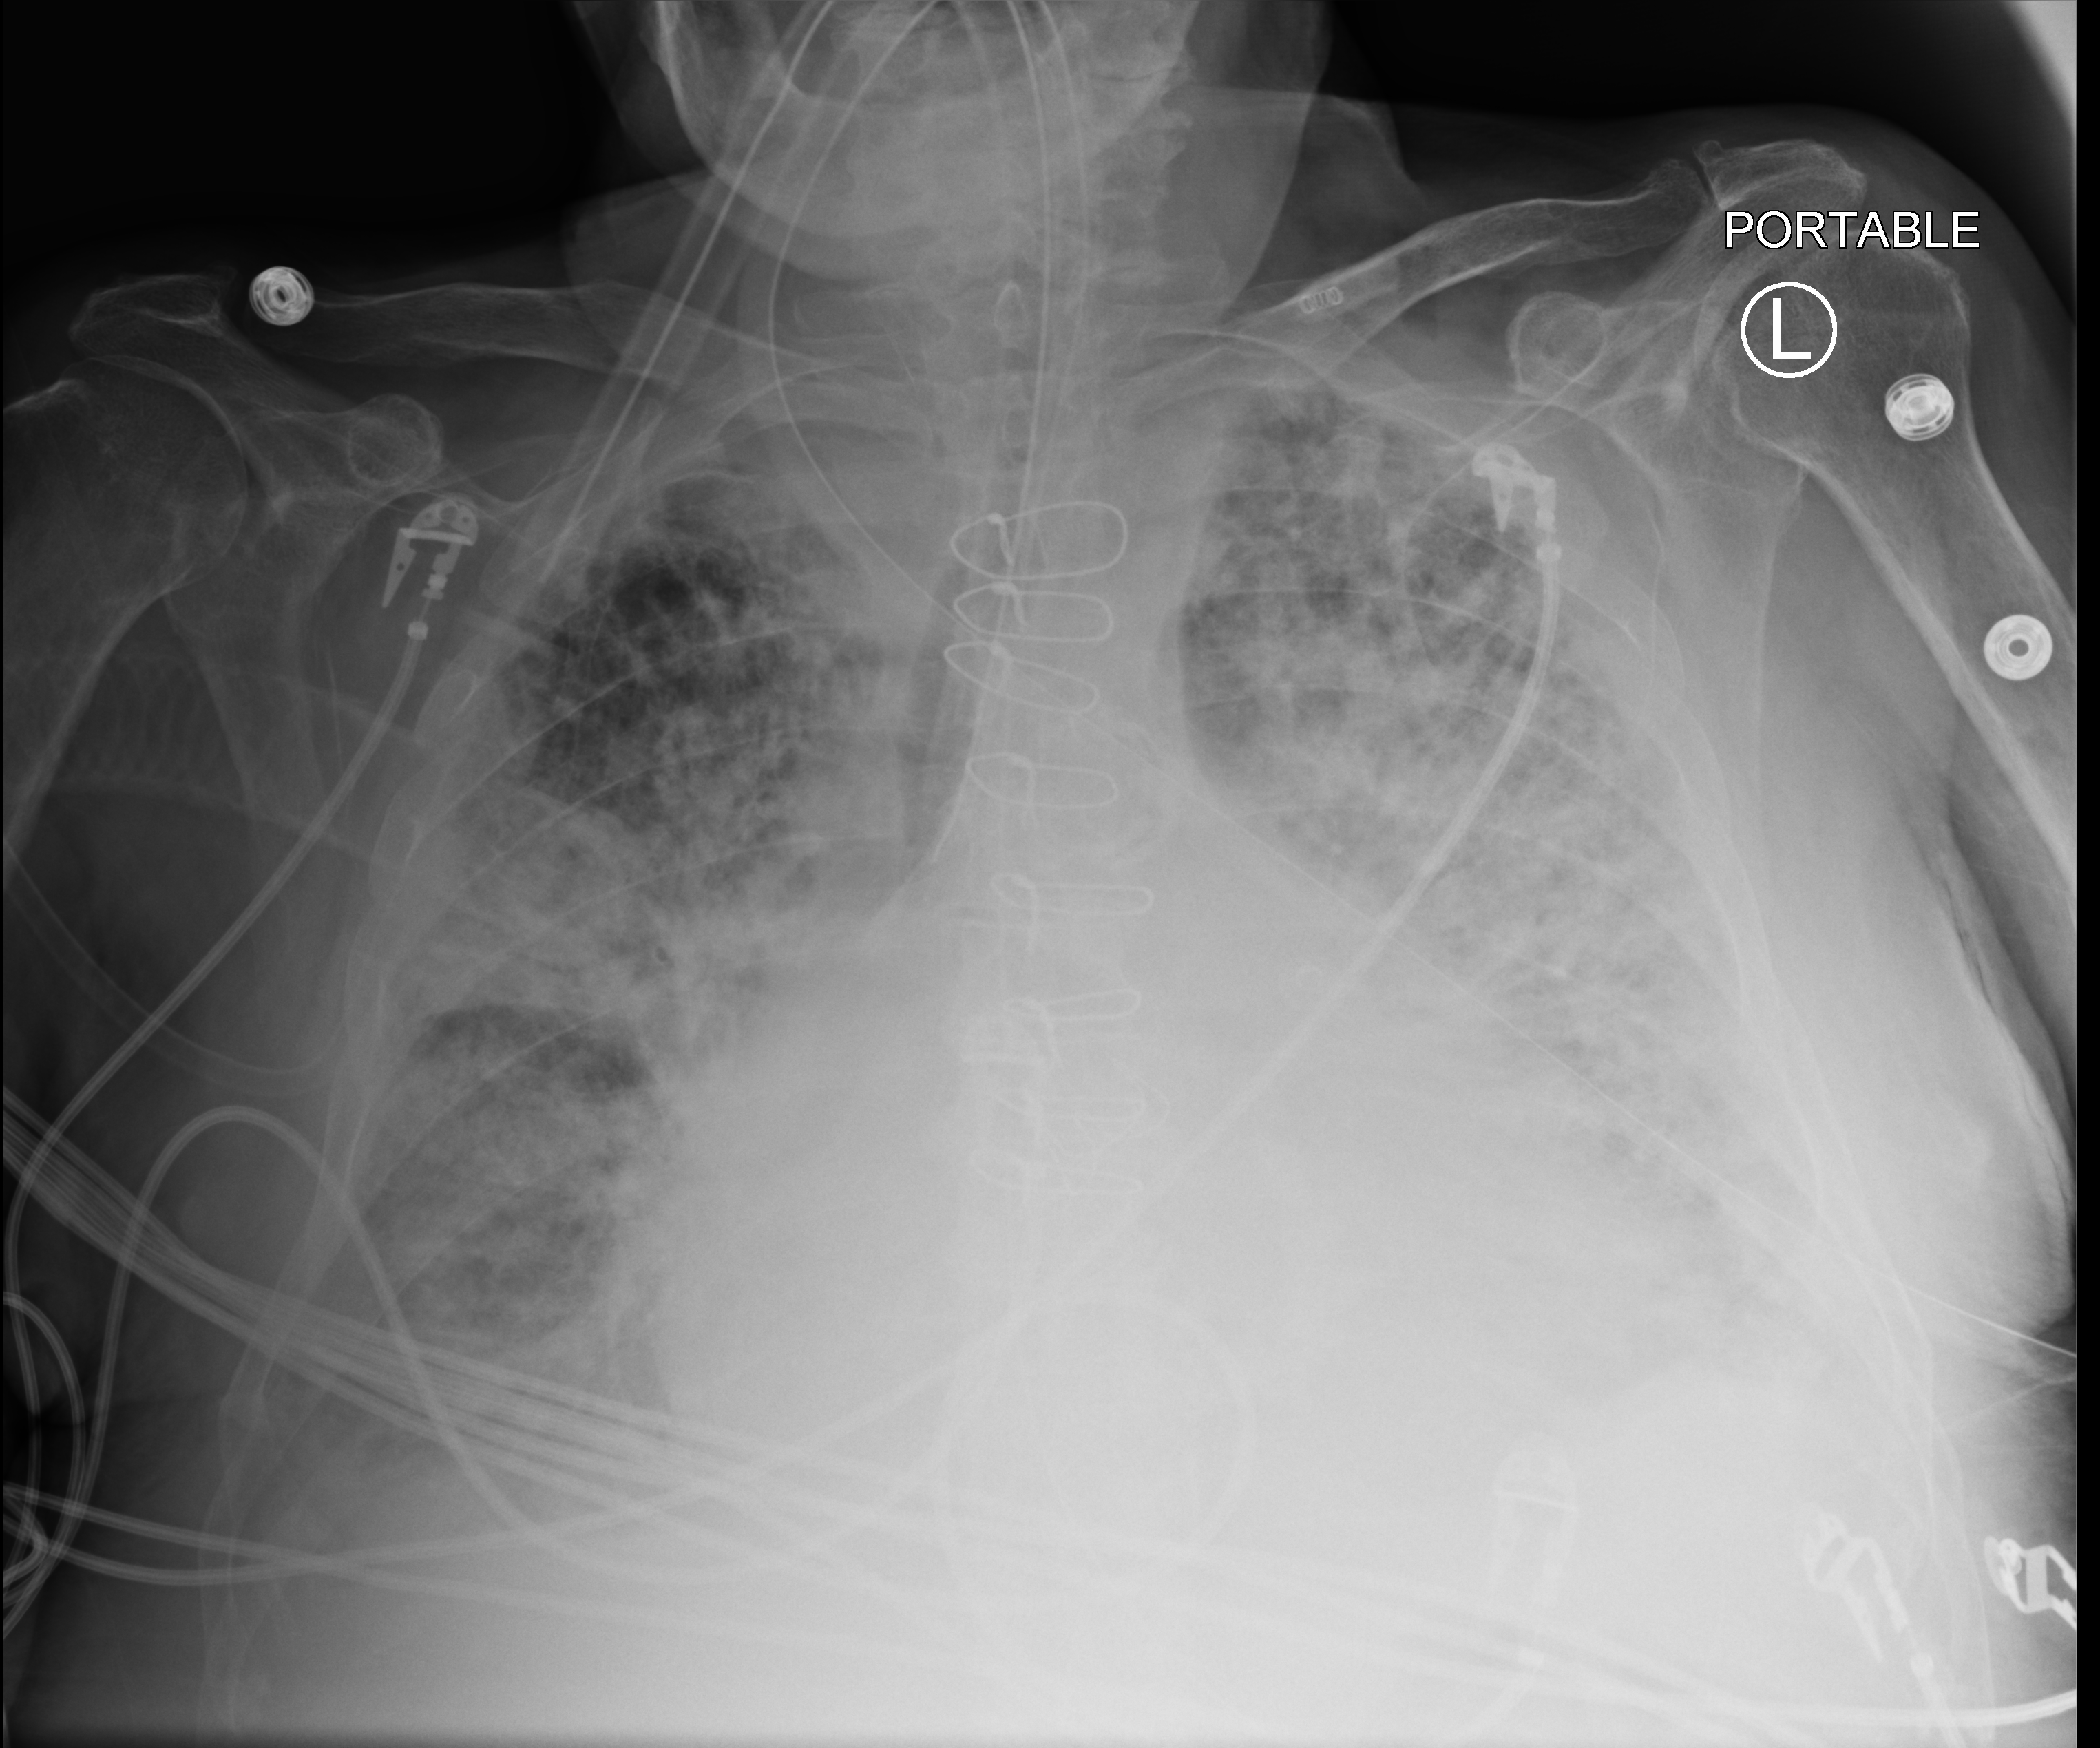
Chest X-ray (portable), anteroposterior (AP) projection. Male patient hospitalised with COVID-19, age 75–90 years.
From the hospital-stay record, not from the radiograph (when in the stay this image was taken is not recorded):
- admitted to intensive care during this hospital stay: yes